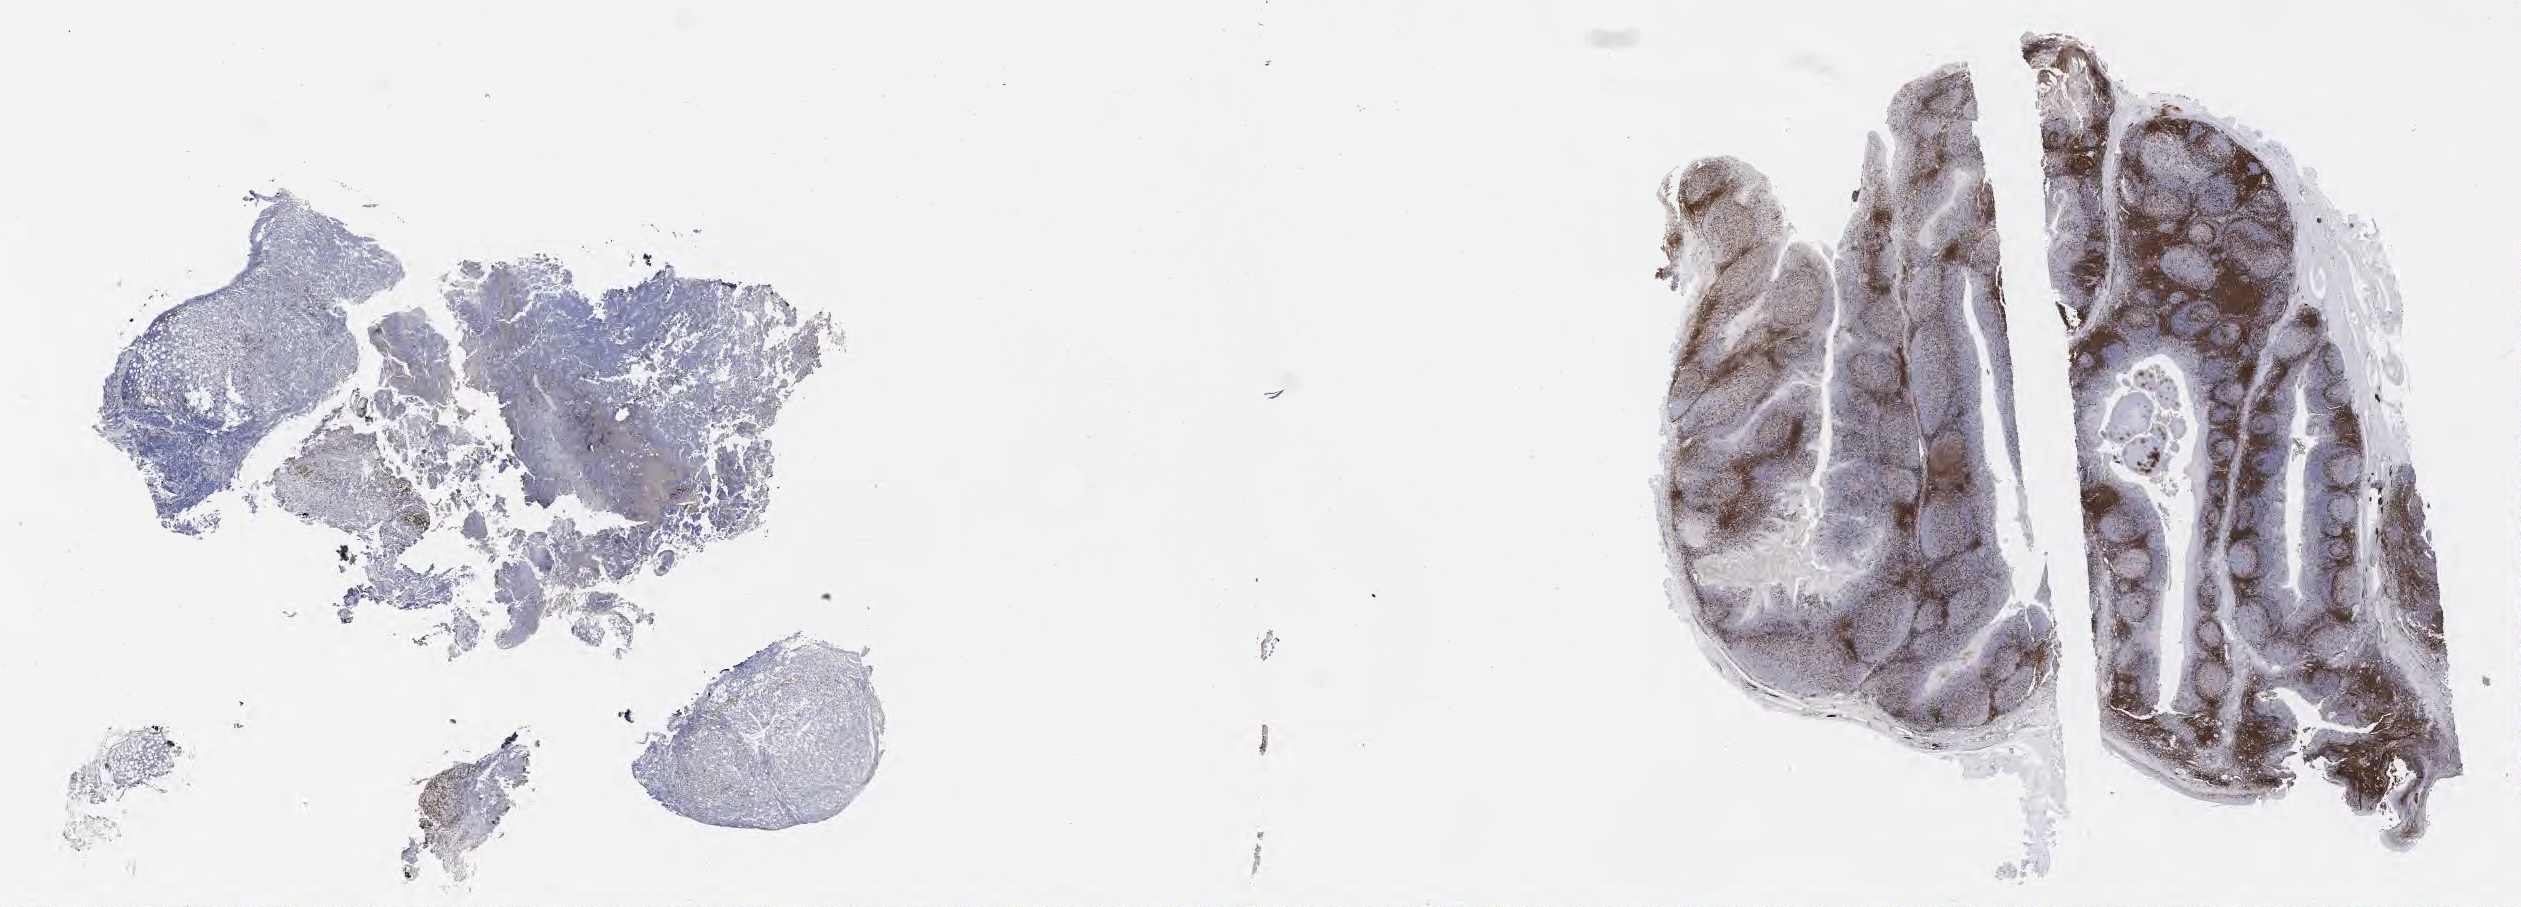
IHC for CD3, whole-slide image, a low-resolution overview of the entire scanned area, about 40.8 x 14.7 mm; specimen: tumor tissue. Male patient, 23 years old.
Histologic diagnosis: Burkitt lymphoma, NOS.